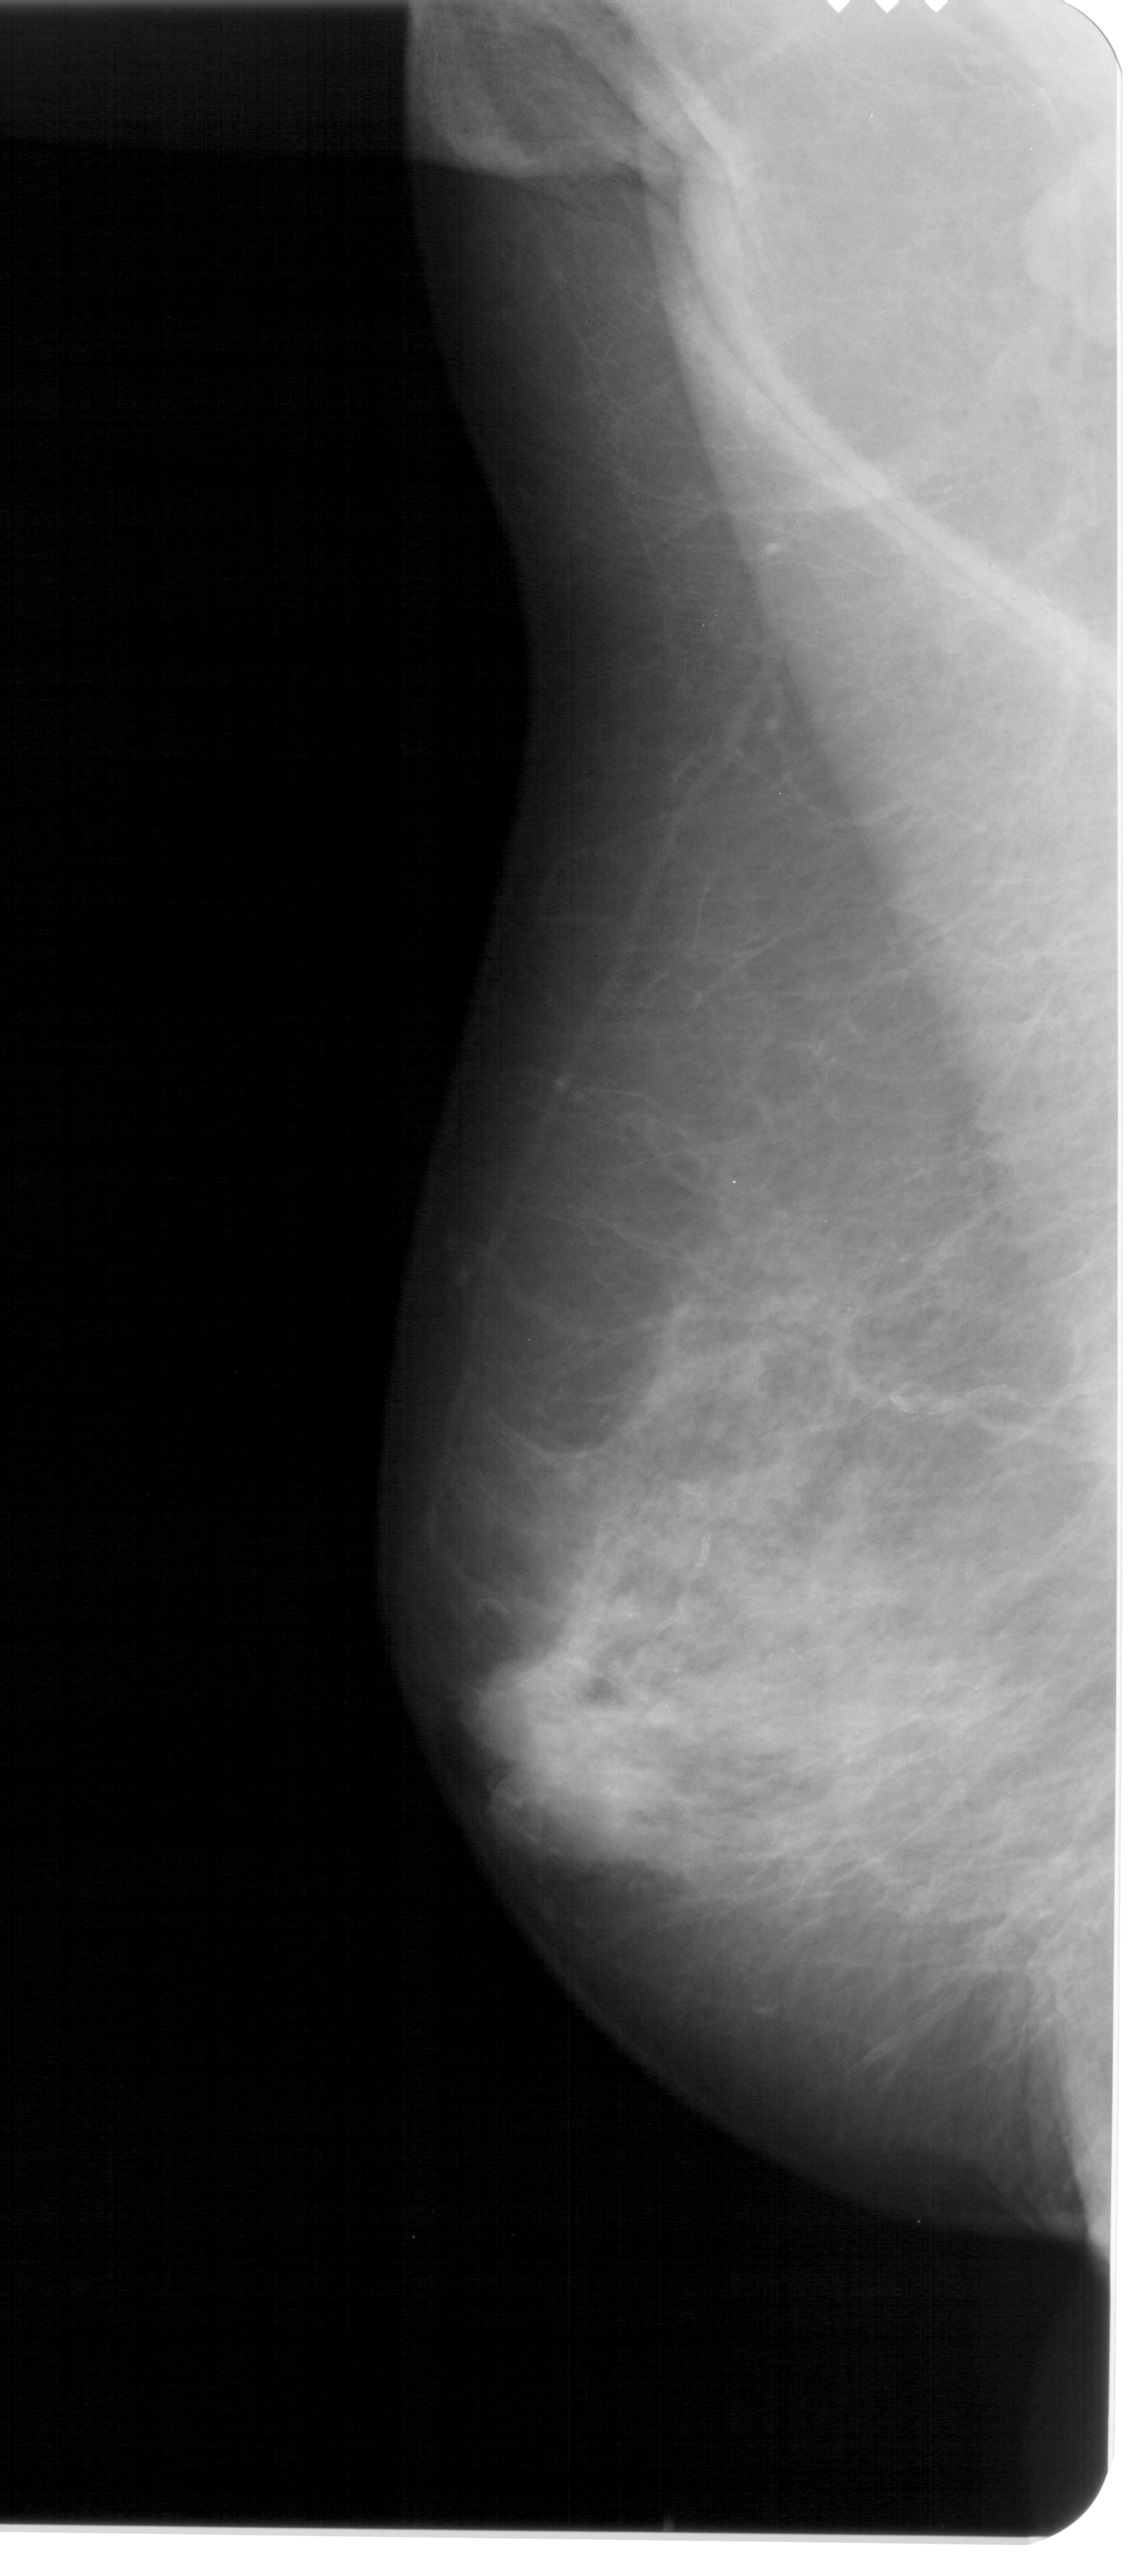
Scanned film-screen mammogram. Left breast. MLO view. BI-RADS breast density category 4 (scale 1–4). 1133 × 2576 image matrix.
Marked abnormalities (boxes around the expert regions of interest):
- calcifications, morphology punctate / amorphous, distribution regional; BI-RADS assessment category 4; subtlety rating 3 on a 1 (subtle) to 5 (obvious) scale; pathology result (as recorded, not read from the image): benign: bounding box <483,1499,912,1913> (left, top, right, bottom; pixels)